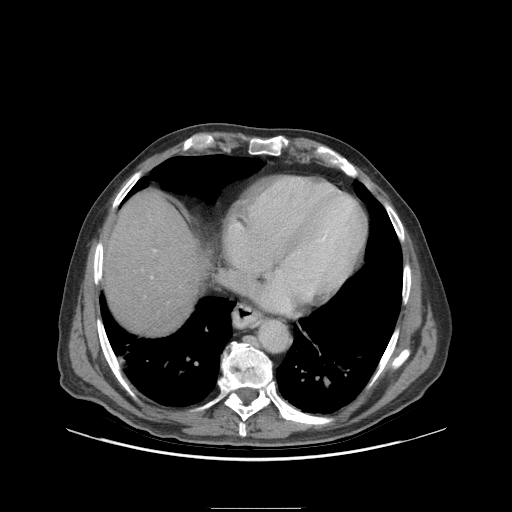
Contrast-enhanced abdominal CT (liver protocol), one axial slice; position 89 of 105 along the scan axis; 140 kVp; soft-tissue window (W 400 / L 40 HU); 2.5 mm slice thickness; 512 × 512 image matrix. Case-level facts recorded for this patient, not image findings: diagnosis: hepatocellular carcinoma (patient treated with transarterial chemoembolisation; whether this scan precedes or follows treatment is not stated here); TNM stage (as recorded): Stage-I; Child-Pugh class: A.
Annotated regions visible in this slice (semi-automatic segmentation, software-assisted and operator-edited):
- liver parenchyma outside the tumour (the mass and vessels are separate outlines, so this box may not span the whole liver): bounding box [x1, y1, x2, y2] px = [102, 192, 202, 334]